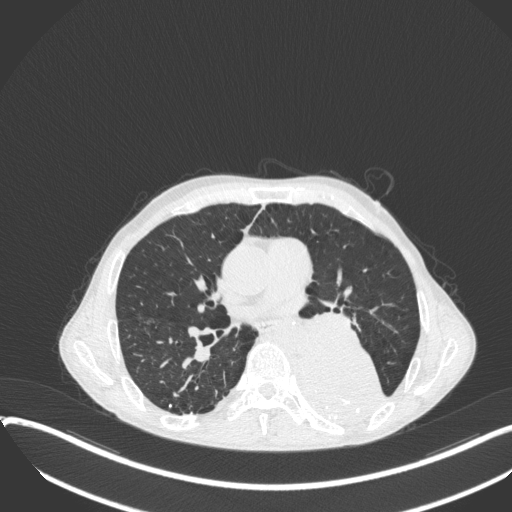
Chest CT, one axial slice; slice 196 of 400 in the series (ordered by position); reconstruction kernel B31f; lung window (W 1500 / L -600 HU); 1 mm slice thickness; 512 × 512 image matrix, field of view 400 × 400 mm. Patient: male, 57 years. Case-level facts recorded for this patient, not image findings: clinical TNM (as recorded): T4 N0 M0.
Annotated regions visible in this slice (bounding box drawn by a radiologist):
- lung tumour (recorded histology: squamous cell carcinoma): bounding box <283,332,387,421> (left, top, right, bottom; pixels)